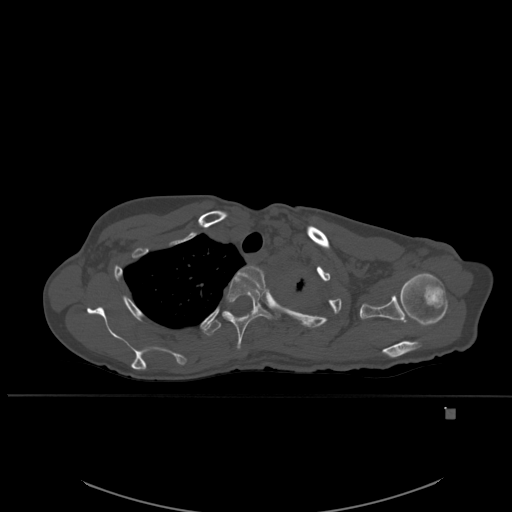
CT including the spine, one axial slice; slice 424 of 537 in the series (ordered by position); bone window (W 1800 / L 400 HU); 1.5 mm slice thickness; 512 × 512 image matrix. Female patient, age 45 years. Case-level facts recorded for this patient, not image findings: primary cancer: lung.
Structures marked on this image (semi-automatically segmented with operator editing):
- T2 vertebra: bounding box [x1, y1, x2, y2] px = [235, 265, 266, 294]
- T3 vertebra: [224, 275, 273, 350]
- T4 vertebra: [202, 310, 229, 336]